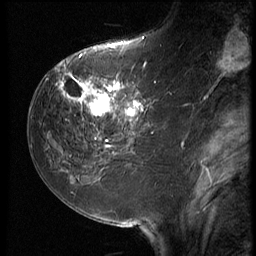
Breast MRI (dynamic contrast-enhanced), one sagittal slice; position 24 of 64 along the scan axis; 3 images stored at this slice position (order not interpretable as contrast timing); 1.5 T; TE 4.2 ms, TR 9 ms; 2.5 mm slice thickness; 256 × 256 image matrix, field of view 180 × 180 mm. Patient: female, 59 years. From the clinical record (not read from this slice): setting: breast cancer imaged before/during neoadjuvant chemotherapy; receptor status: HER2-positive.
Structures marked on this image (semi-automatic segmentation, software-assisted and operator-edited):
- analysis volume of interest (the breast-tissue region the enhancement analysis was run in; not a lesion): bounding box [x1, y1, x2, y2] px = [54, 65, 155, 132]
- tumour enhancement mask (voxels above the 140 % enhancement threshold inside the analysis volume of interest): [58, 65, 150, 127]